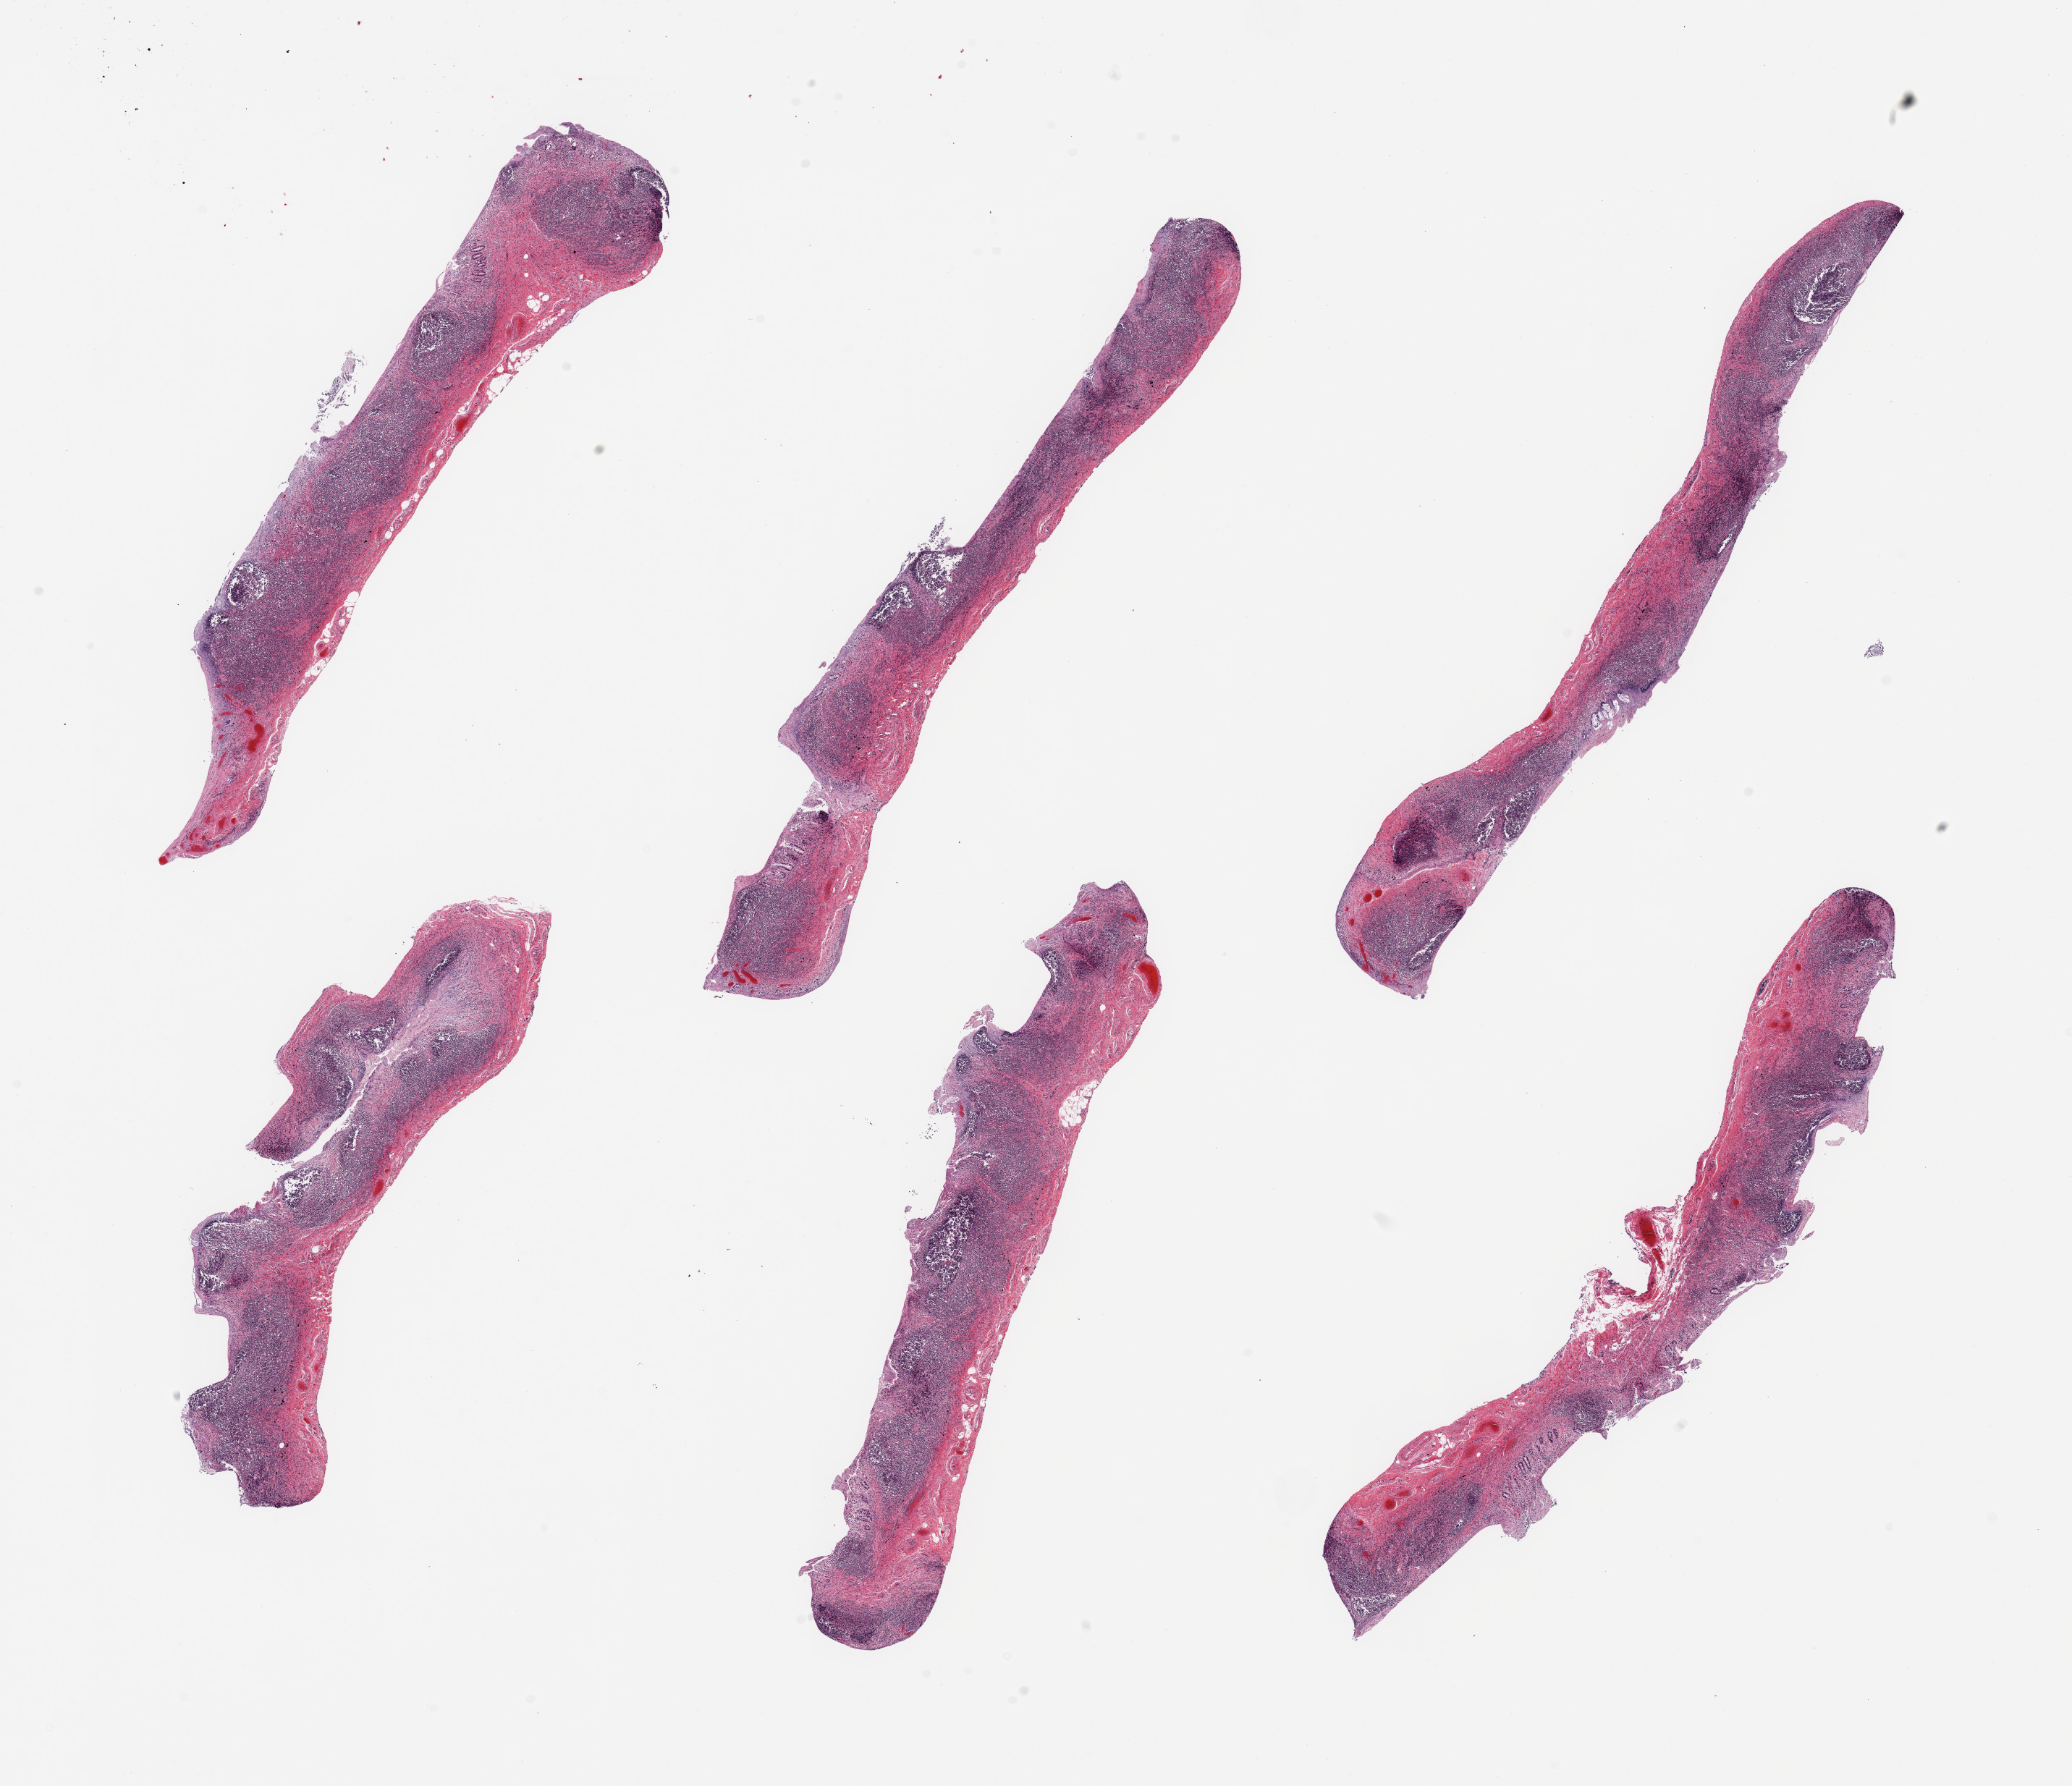
Hematoxylin and eosin (H&E) whole-slide image, a low-resolution overview of the entire scanned area, about 22.6 x 19.5 mm (acquisition: 20x scan), PAXgene-fixed paraffin-embedded (PFPE) section, section of ileum (target tissue), tissue donor sample. Donor sex: male.
- pathologist's review note for this sample: 6 pieces, glandular mucosa autolyzed; residual target lymphoid aggregates are ~40% remaining tissue